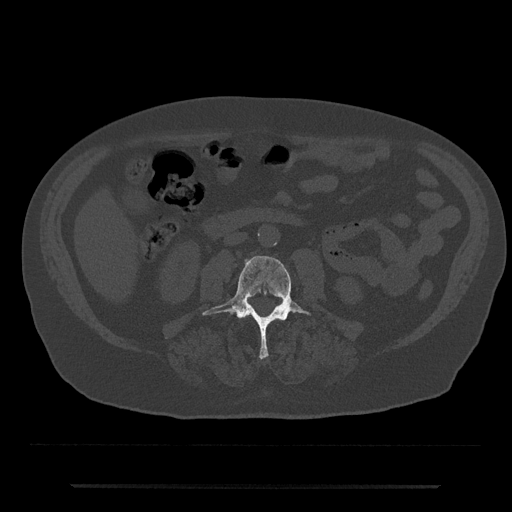
CT including the spine, one axial slice; position 411 of 797 along the scan axis; bone window (W 1800 / L 400 HU); 0.5 mm slice thickness; 512 × 512 image matrix, field of view 434 × 434 mm. Patient: male, 80 years. Case-level facts recorded for this patient, not image findings: primary cancer: prostate; vertebrae with lytic lesions (as recorded): L1, T11.
Outlined on this slice (semi-automatic segmentation, software-assisted and operator-edited):
- L3 vertebra: bounding box (x1, y1, x2, y2) in pixels: (203, 256, 310, 360)